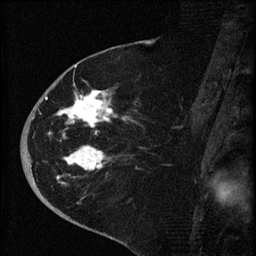
Breast MRI (dynamic contrast-enhanced), one sagittal slice. Slice 32 of 60 in the series (ordered by position). Dynamic contrast-enhanced series, image 2 of 4 at this slice position (ordered by acquisition). 1.5 T. TE 4.2 ms, TR 8.2 ms. 2 mm slice thickness. 256 × 256 image matrix, field of view 180 × 180 mm. Female patient, age 71 years.
Annotated regions visible in this slice (semi-automatically segmented with operator editing):
- analysis volume of interest (the breast-tissue region the enhancement analysis was run in; not a lesion): bounding box (x1, y1, x2, y2) in pixels: (35, 75, 143, 190)
- tumour enhancement mask (voxels above the 70 % enhancement threshold inside the analysis volume of interest): (35, 90, 127, 180)